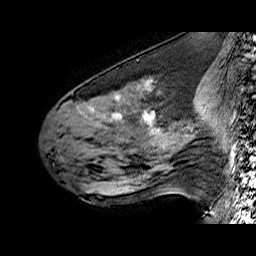
Breast MRI (dynamic contrast-enhanced), one sagittal slice; position 25 of 60 along the scan axis; dynamic contrast-enhanced series, time point 2 of 6 at this slice position (early post-contrast); 1.5 T; TE 6.4 ms, TR 32.9 ms; 4 mm slice thickness; 256 × 256 image matrix. Female patient. Case-level facts recorded for this patient, not image findings: setting: breast cancer imaged before/during neoadjuvant chemotherapy; receptor status: HER2-positive.
Structures marked on this image (semi-automatically segmented with operator editing):
- analysis volume of interest (the breast-tissue region the enhancement analysis was run in; not a lesion): bounding box (x1, y1, x2, y2) in pixels: (51, 78, 196, 160)
- tumour enhancement mask (voxels above the 100 % enhancement threshold inside the analysis volume of interest): (91, 81, 156, 134)